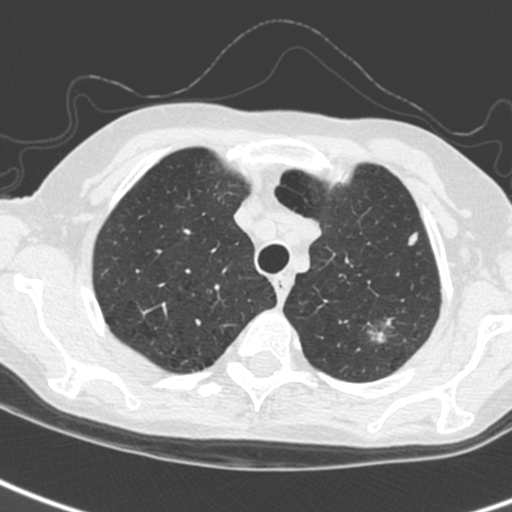
Axial slice from a low-dose chest CT screening exam. First (baseline) screen. Lung window (W 1500 / L -600 HU). 1.3 mm slice thickness. Slice 33 of 242 in the series. Female, age 61 years at enrolment. Current smoker at enrolment.
2 expert-annotated lung lesions on this slice (largest first), bounding box <355,309,412,353> (left, top, right, bottom; pixels); <394,224,431,257>. The screening reader recorded 2 non-calcified nodules or masses ≥4 mm on this exam; which of them these boxes mark is not recorded. Official screen result: positive, change unspecified: nodule(s) >= 4 mm or enlarging nodule(s), mass(es), or other non-specific abnormalities suspicious for lung cancer. Lung cancer was diagnosed 29 days after this screen: small cell carcinoma, NOS, left upper lobe, stage IV (AJCC 6th edition).